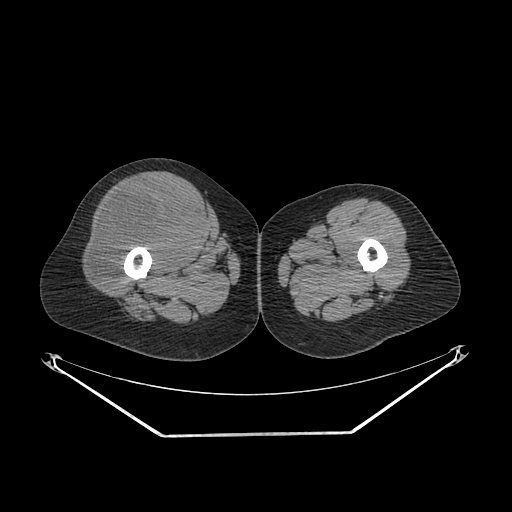
CT of an extremity soft-tissue mass (from a PET/CT study), one axial slice. Slice 252 of 311 in the series (ordered by position). 140 kVp. Soft-tissue window (W 400 / L 40 HU). 3.75 mm slice thickness. 512 × 512 image matrix, field of view 500 × 500 mm. Female patient. From the clinical record (not read from this slice): histological type: pleiomorphic undifferentiated sarcoma; grade: high; site of the primary tumour: right quadricep.
Annotated regions visible in this slice (expert contour drawn on MRI and transferred to this co-registered scan by the dataset authors):
- tumour plus oedema (research contour): bounding box <93,183,200,289> (left, top, right, bottom; pixels)
- tumour (research contour): <93,183,200,289>